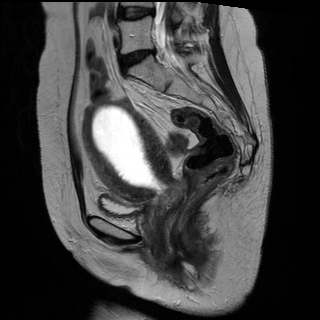
Pelvic MRI for cervical cancer, one sagittal slice. Slice 14 of 29 in the series (ordered by position). T2-weighted. 1.5 T. TE 89 ms, TR 2930 ms. 320 × 320 image matrix, field of view 260 × 260 mm. Female patient, age 49 years.
Outlined on this slice (manually delineated by an expert):
- uterus and cervix: box from (x=81, y=98) to (x=189, y=217) px